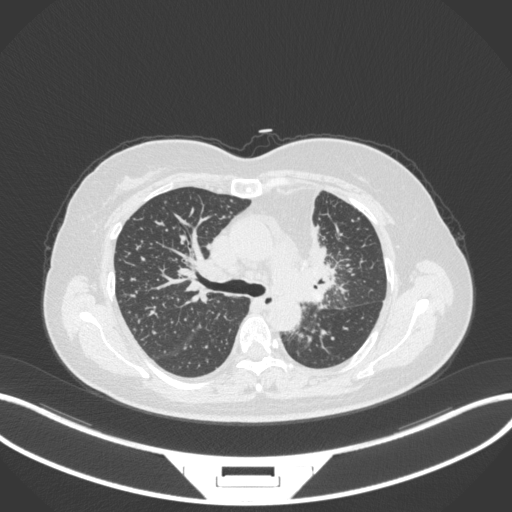
Chest CT, one axial slice; slice 217 of 348 in the series (ordered by position); lung window (W 1500 / L -600 HU); 1 mm slice thickness; 512 × 512 image matrix, field of view 400 × 400 mm. Patient: female, 49 years. Case-level facts recorded for this patient, not image findings: clinical TNM (as recorded): T1c N0 M1.
Structures marked on this image (bounding box drawn by a radiologist):
- lung tumour (recorded histology: adenocarcinoma): bounding box <298,187,340,305> (left, top, right, bottom; pixels)